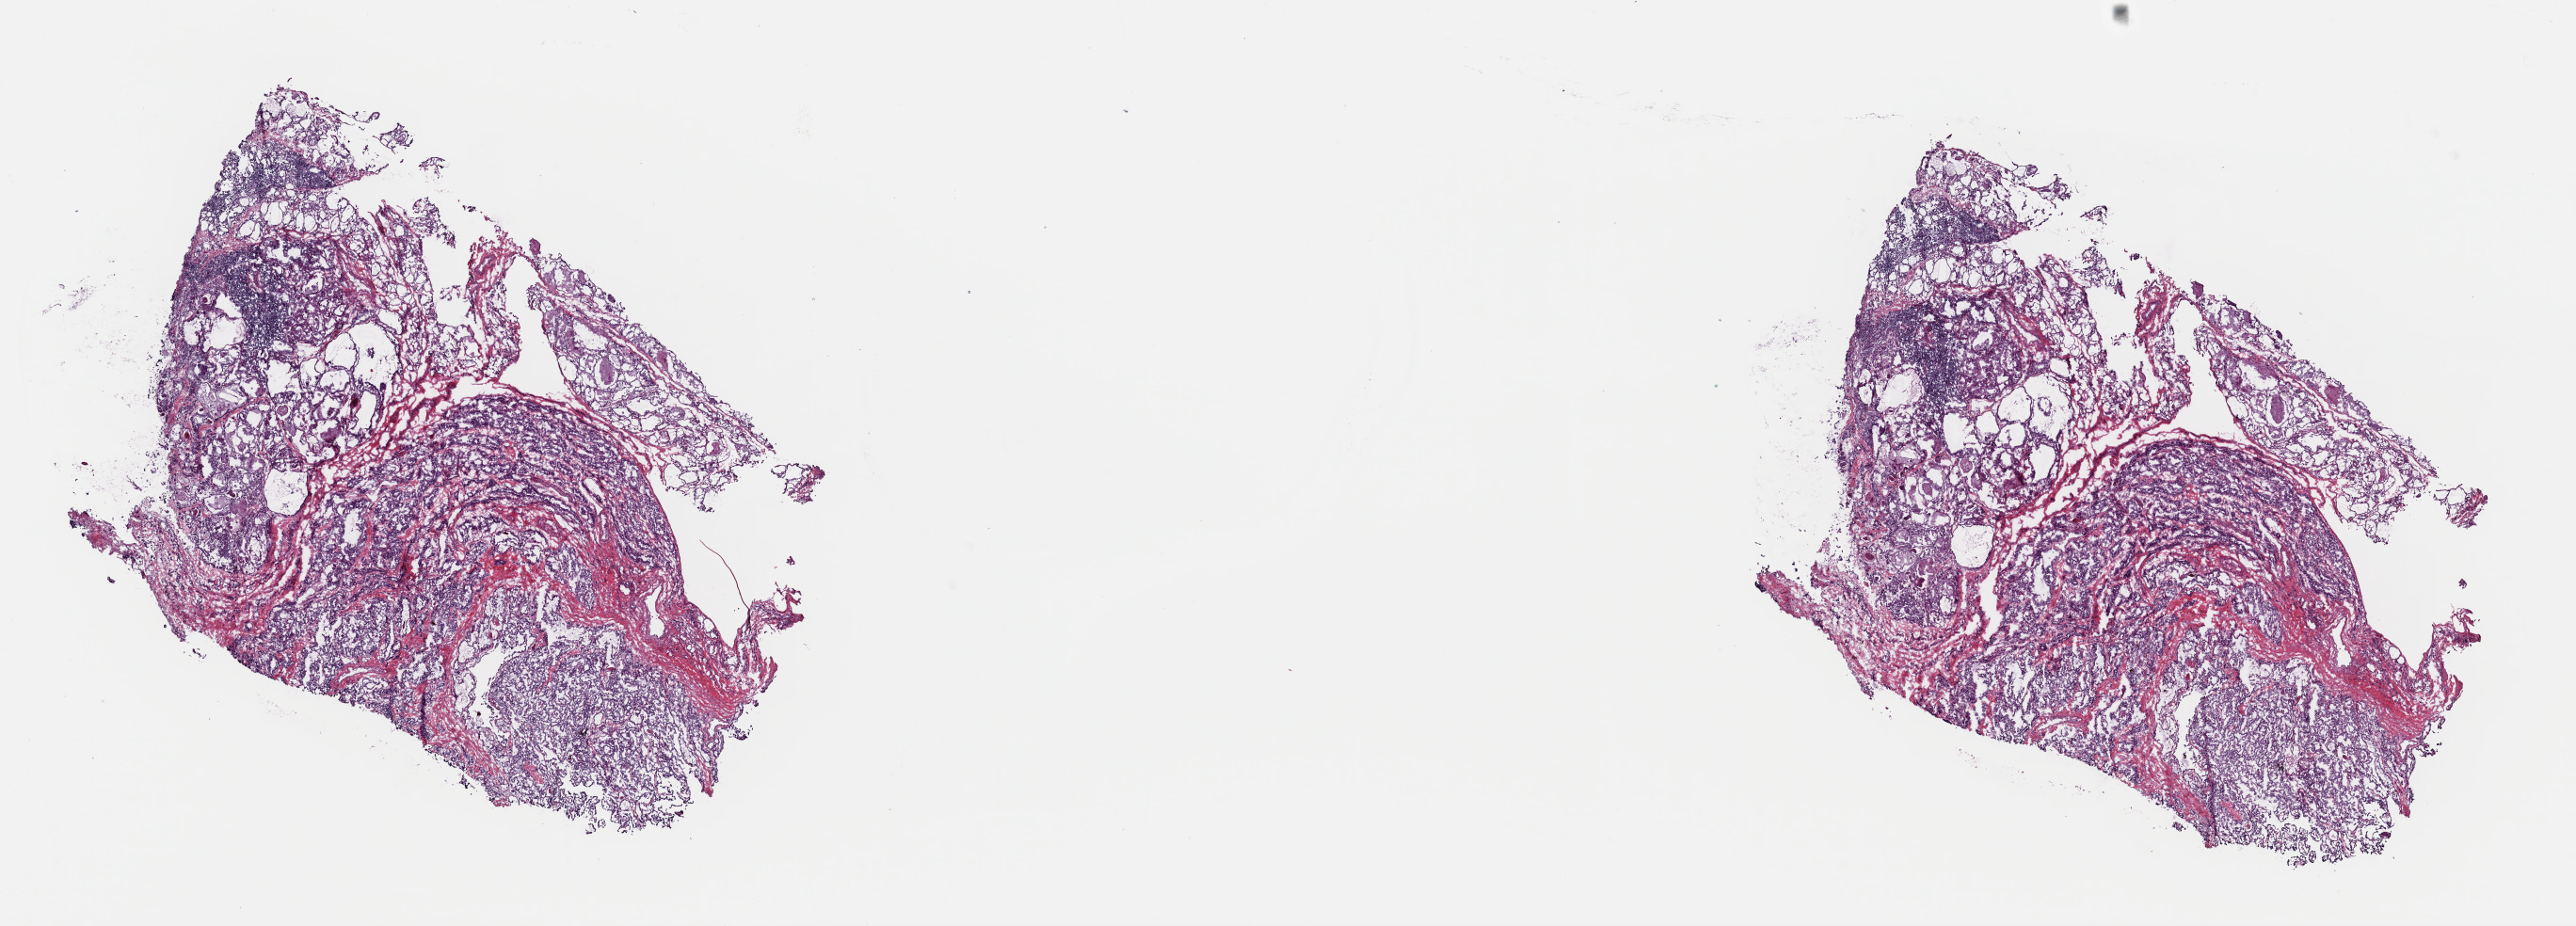
H&E-stained whole-slide image, shown as a low-resolution overview of the whole scanned area (about 21.6 x 7.8 mm); frozen section from the top of the tissue portion; primary tumour sample from the thyroid. Female patient; age at initial diagnosis 45 years. Pathologist review of this section (percent, as recorded): tumour cells 50%, tumour nuclei 60%, normal cells 50%, stromal cells 0%, necrosis 0%. Infiltration values recorded for this section: lymphocyte infiltration 0%, monocyte infiltration 0%, neutrophil infiltration 0%.
* histologic diagnosis: Papillary adenocarcinoma, NOS
* laterality: right
* AJCC pathologic stage: III (5th edition)
* lymph nodes positive (case pathology): 10 of 21 examined